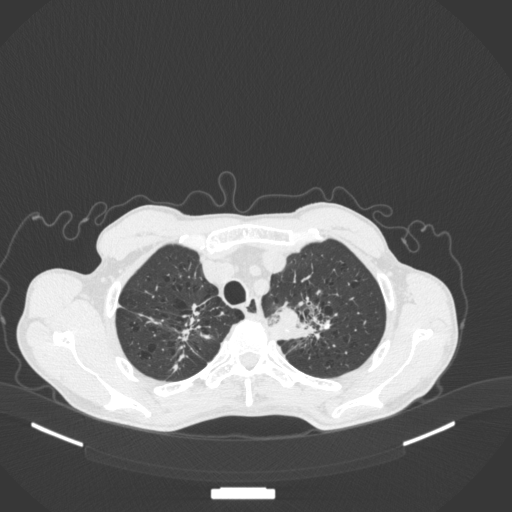
Chest CT, one axial slice. Position 360 of 394 along the scan axis. Reconstruction kernel B31f. 120 kVp. Lung window (W 1500 / L -600 HU). 512 × 512 image matrix, field of view 400 × 400 mm. Male patient, age 65 years. From the clinical record (not read from this slice): clinical TNM (as recorded): T2b N0 M0.
Annotated regions visible in this slice (rectangle marked by the reading radiologist):
- lung tumour (recorded histology: adenocarcinoma): bounding box <266,297,306,331> (left, top, right, bottom; pixels)